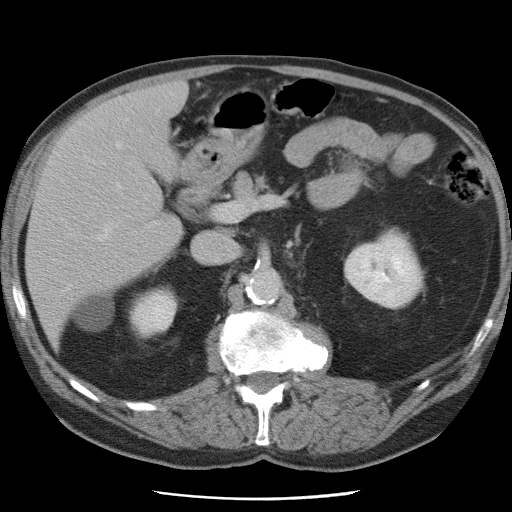
Contrast-enhanced abdominal CT, one axial slice; slice 39 of 78 in the series (ordered by position); intravenous contrast given; soft-tissue window (W 400 / L 40 HU); 5 mm slice thickness; 512 × 512 image matrix, field of view 337 × 337 mm. Male patient, age 75 years. From the clinical record (not read from this slice): diagnosis: colorectal cancer liver metastases, imaged before liver resection; multiple liver metastases: yes; largest metastasis: 2.4 cm; disease in both lobes: yes.
Outlined on this slice (outlined manually by an expert reader):
- hepatic veins: box from (x=89, y=119) to (x=127, y=241) px
- liver: (x=28, y=83)–(x=187, y=341)
- planned liver remnant (the part of the liver to remain after resection): (x=28, y=118)–(x=181, y=341)
- portal vein (with intrahepatic branches): (x=116, y=184)–(x=120, y=187)